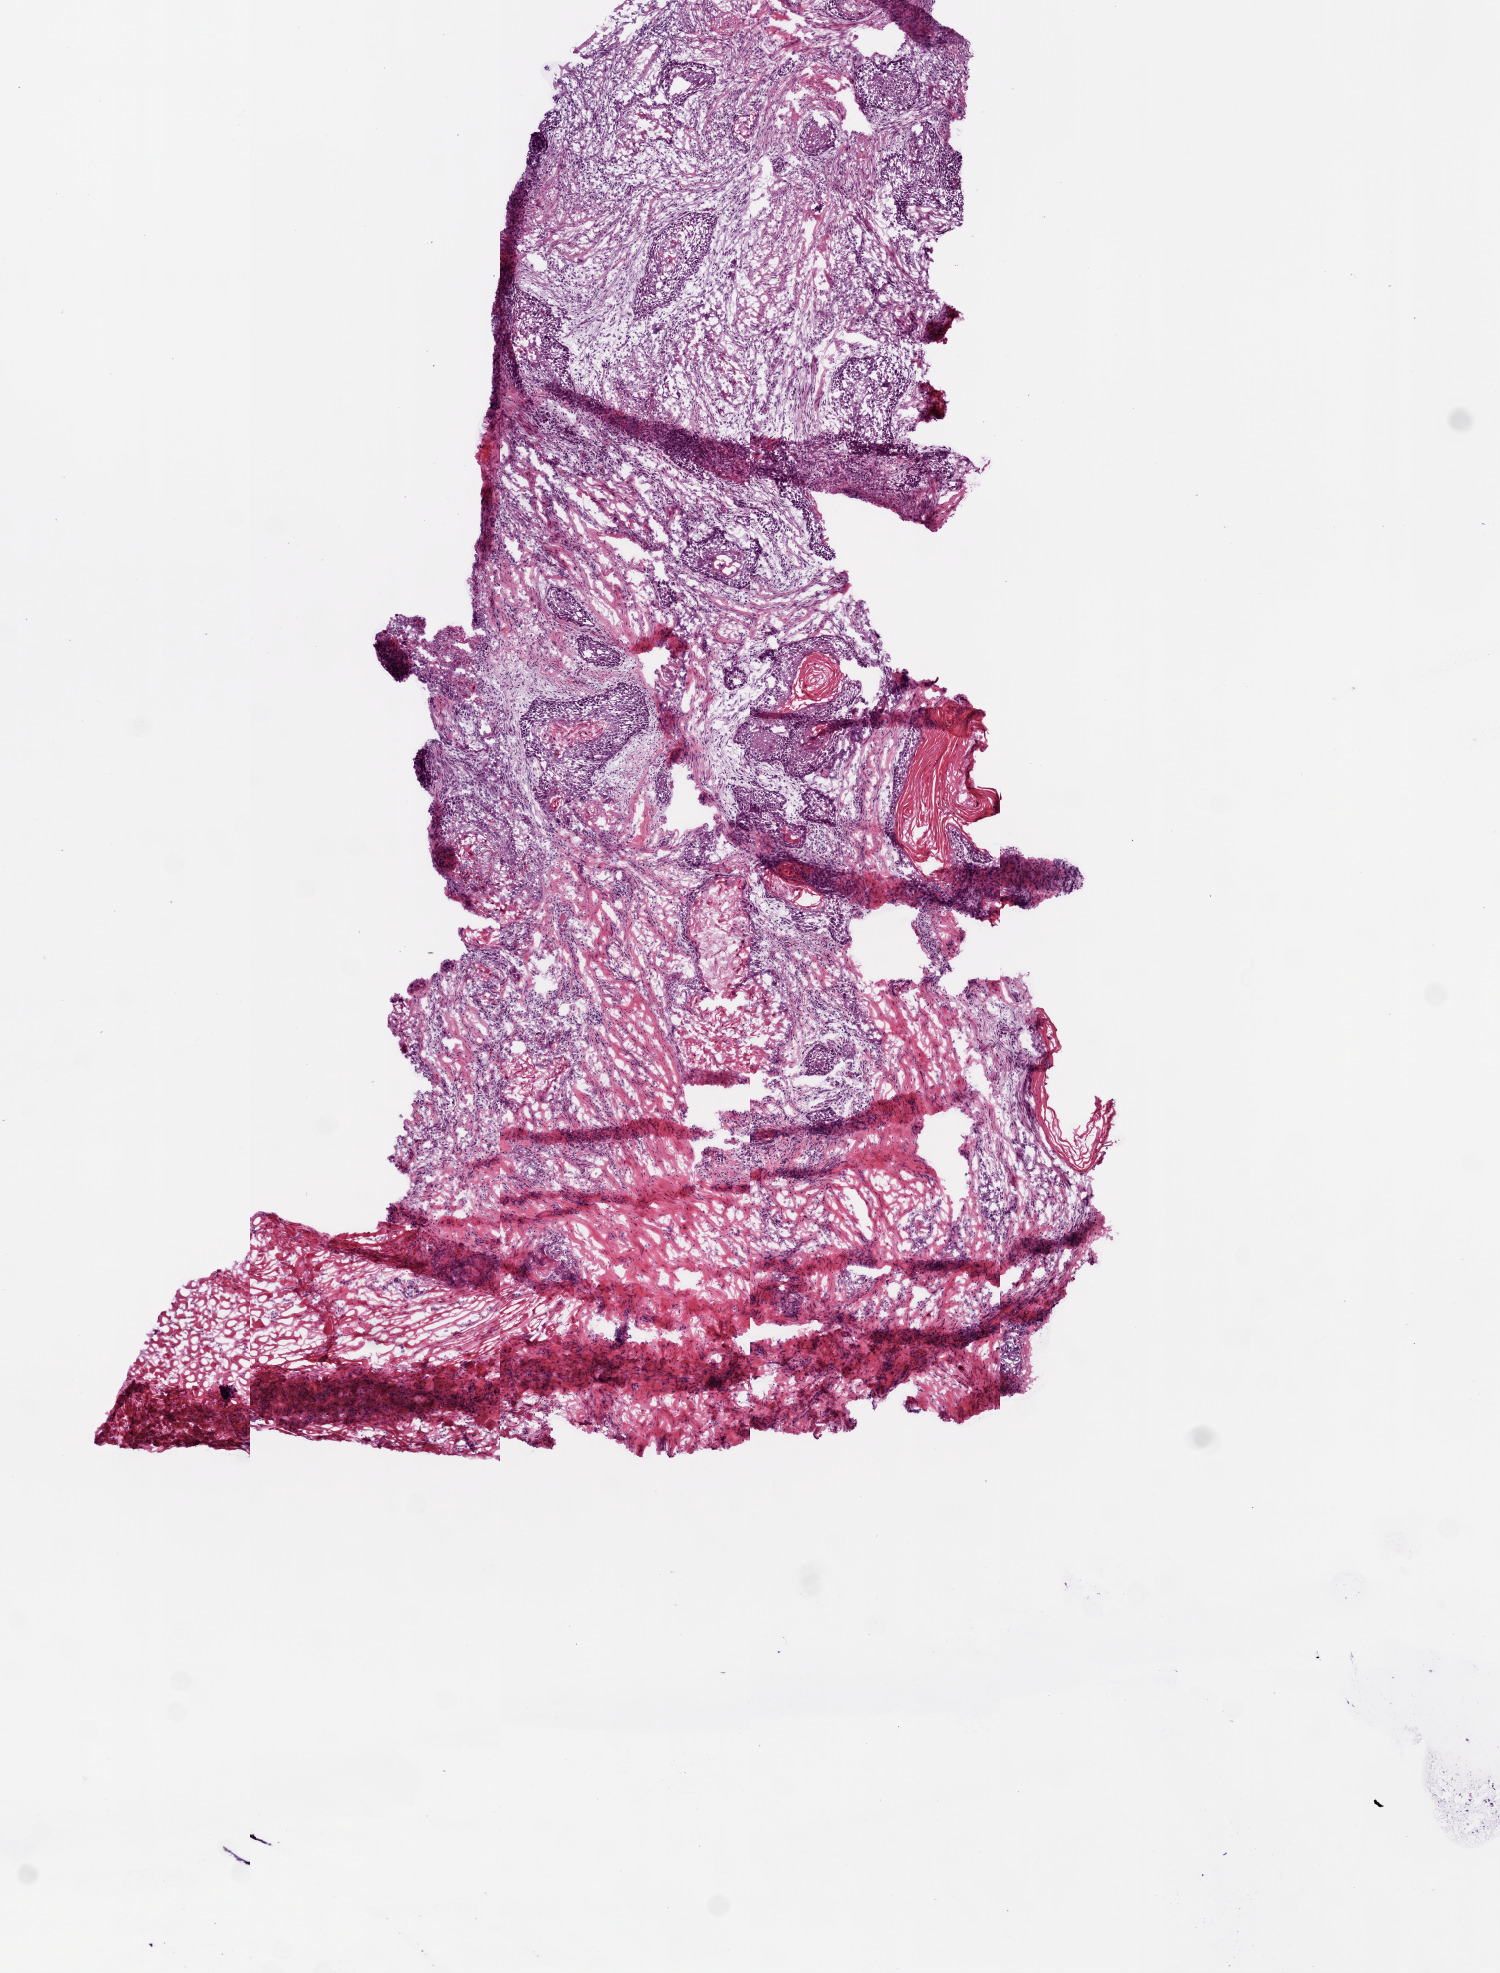
Whole-slide histology image, Hematoxylin and eosin (H&E) stained — a low-resolution overview of the entire scanned area, about 6.0 x 7.9 mm; frozen section from the top of the tissue portion; sample: primary tumour, head and neck. Patient: female, age at initial diagnosis 79 years. Histologic grade: G2 (moderately differentiated). Slide review estimates, as recorded: tumour cells 30%, tumour nuclei 70%, normal cells 0%, stromal cells 70%, necrosis 0%.
* diagnosis: Squamous cell carcinoma, NOS
* AJCC pathologic stage: IVA